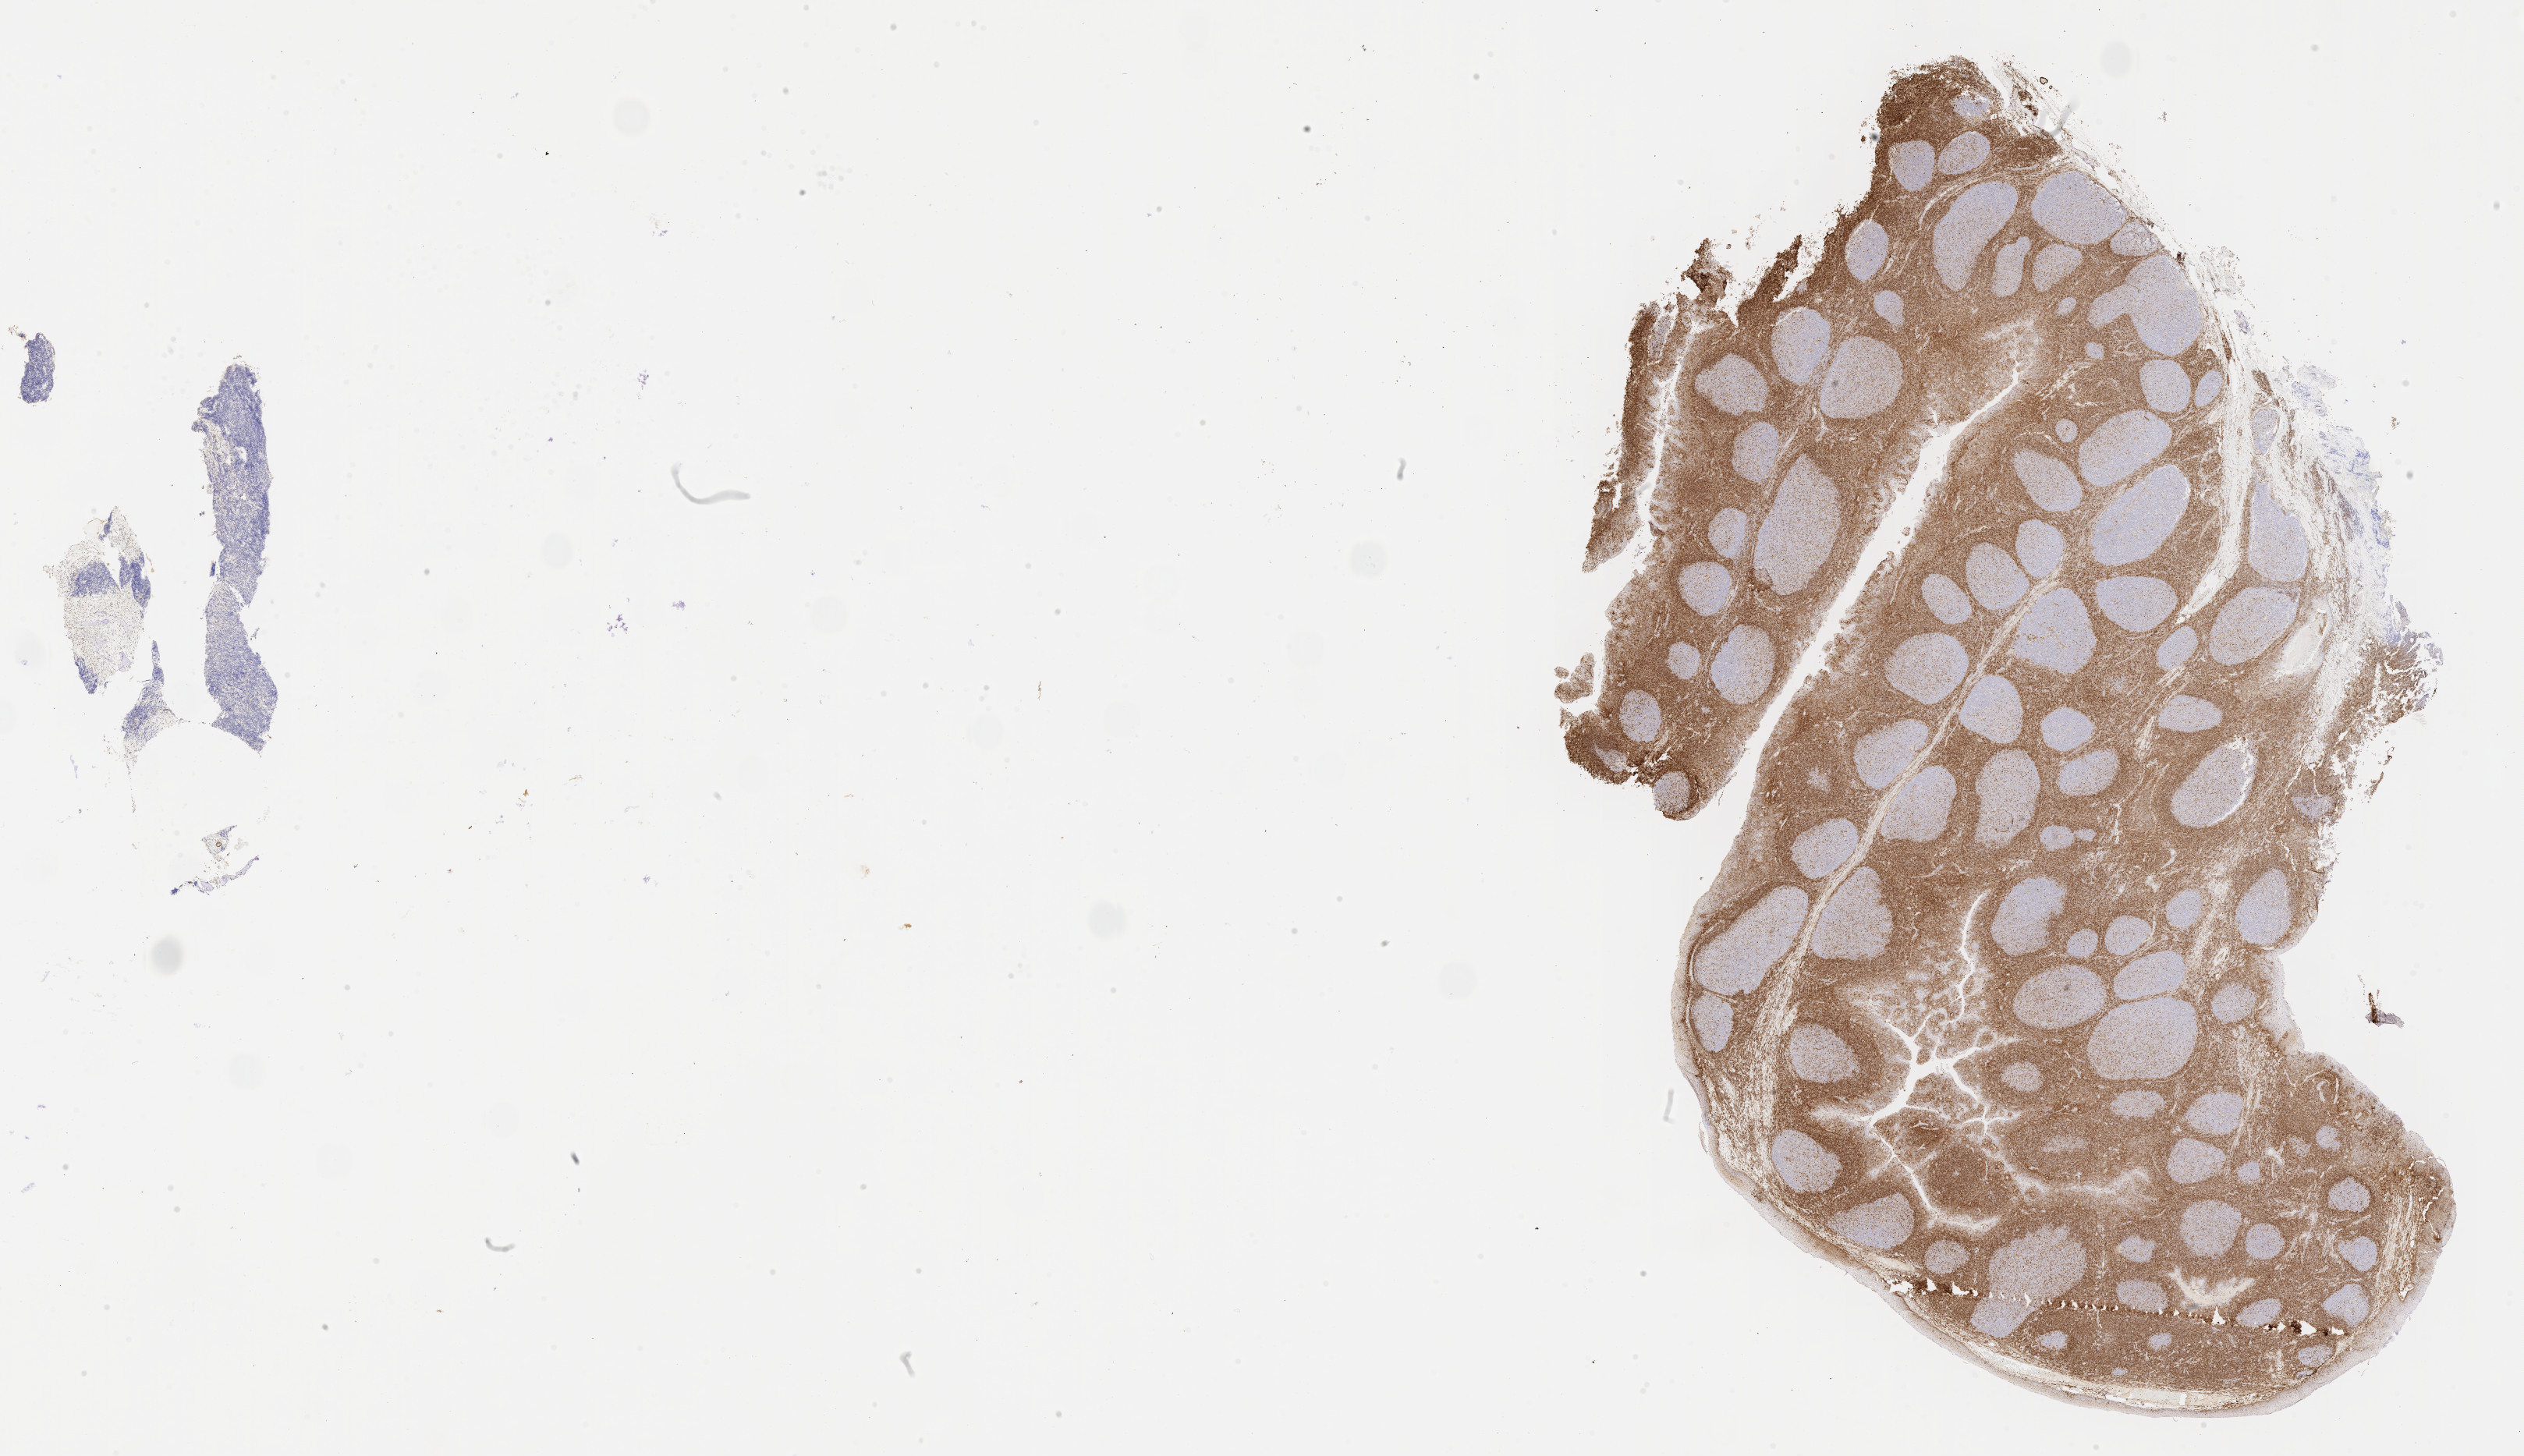
Whole-slide image, immunohistochemical stain for BCL2, whole scanned area (about 26.2 x 15.1 mm) shown as a low-resolution overview. Tumor tissue. Anatomic site: mandible. Patient: male, age at initial diagnosis 6 years.
Diagnosis: Burkitt lymphoma, NOS.